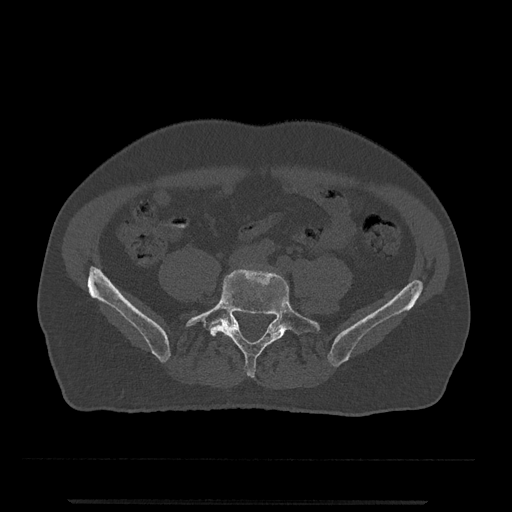
CT including the spine, one axial slice; slice 77 of 797 in the series (ordered by position); reconstruction kernel Br40s/3; 120 kVp; bone window (W 1800 / L 400 HU); 0.5 mm slice thickness; 512 × 512 image matrix, field of view 419 × 419 mm. Patient: male, 63 years. Case-level facts recorded for this patient, not image findings: primary cancer: prostate.
Annotated regions visible in this slice (semi-automatically segmented with operator editing):
- L4 vertebra: box from (x=232, y=320) to (x=234, y=322) px
- L5 vertebra: (x=186, y=269)–(x=321, y=378)